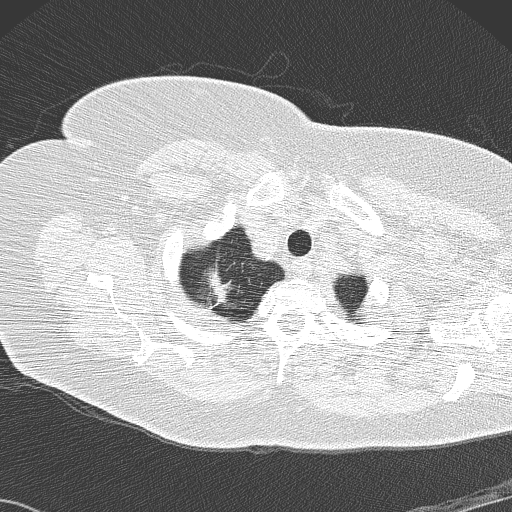
Chest CT (low-dose screening protocol), one axial image, second annual screen, lung window (W 1500 / L -600 HU), slice 15 of 146 in the series, 512 × 512 image matrix, field of view 350 × 350 mm. Female, age 72 years at enrolment. Former smoker at enrolment.
- Expert reader's lesion annotation, bounding box (x1, y1, x2, y2) in pixels: (183, 247, 257, 326).
- The screening reader recorded 4 non-calcified nodules or masses ≥4 mm on this exam; which of them this box marks is not recorded.
- Lung cancer was diagnosed 52 days after this screen: bronchiolo-alveolar adenocarcinoma, NOS, right upper lobe, stage IIIB (AJCC 6th edition), 45 mm at pathology.